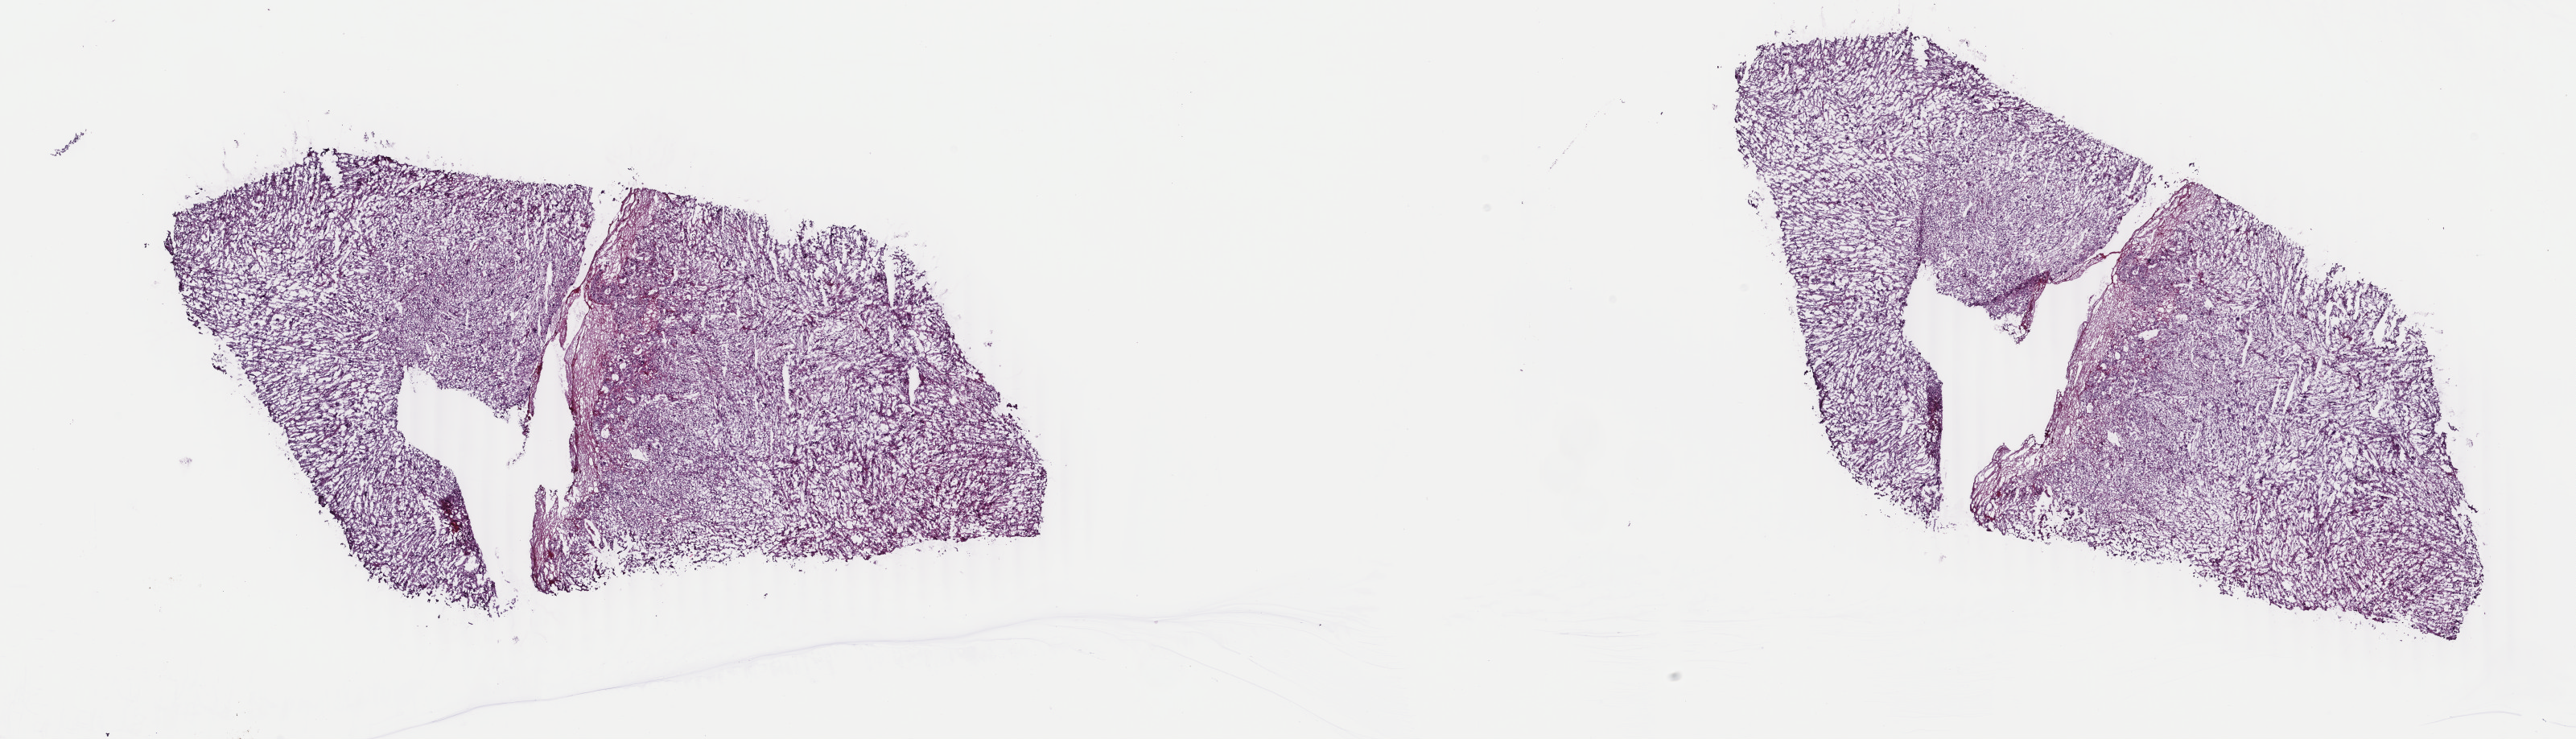
H&E whole-slide image, shown as a low-resolution overview of the whole scanned area (about 25.5 x 7.3 mm, slide scanned at 40x); frozen section; adrenal cortex, primary tumour sample. Male patient; age at initial diagnosis 66 years. Slide review estimates, as recorded: tumour cells 100%, tumour nuclei 80%, normal cells 0%, stromal cells 0%, necrosis 0%. Inflammatory infiltration, as recorded: lymphocyte infiltration 4%, monocyte infiltration 0%, neutrophil infiltration 0%.
• pathologic diagnosis: Adrenal cortical carcinoma (cortex of adrenal gland)
• lymph nodes positive (case pathology): 0 of 1 examined
• laterality: left